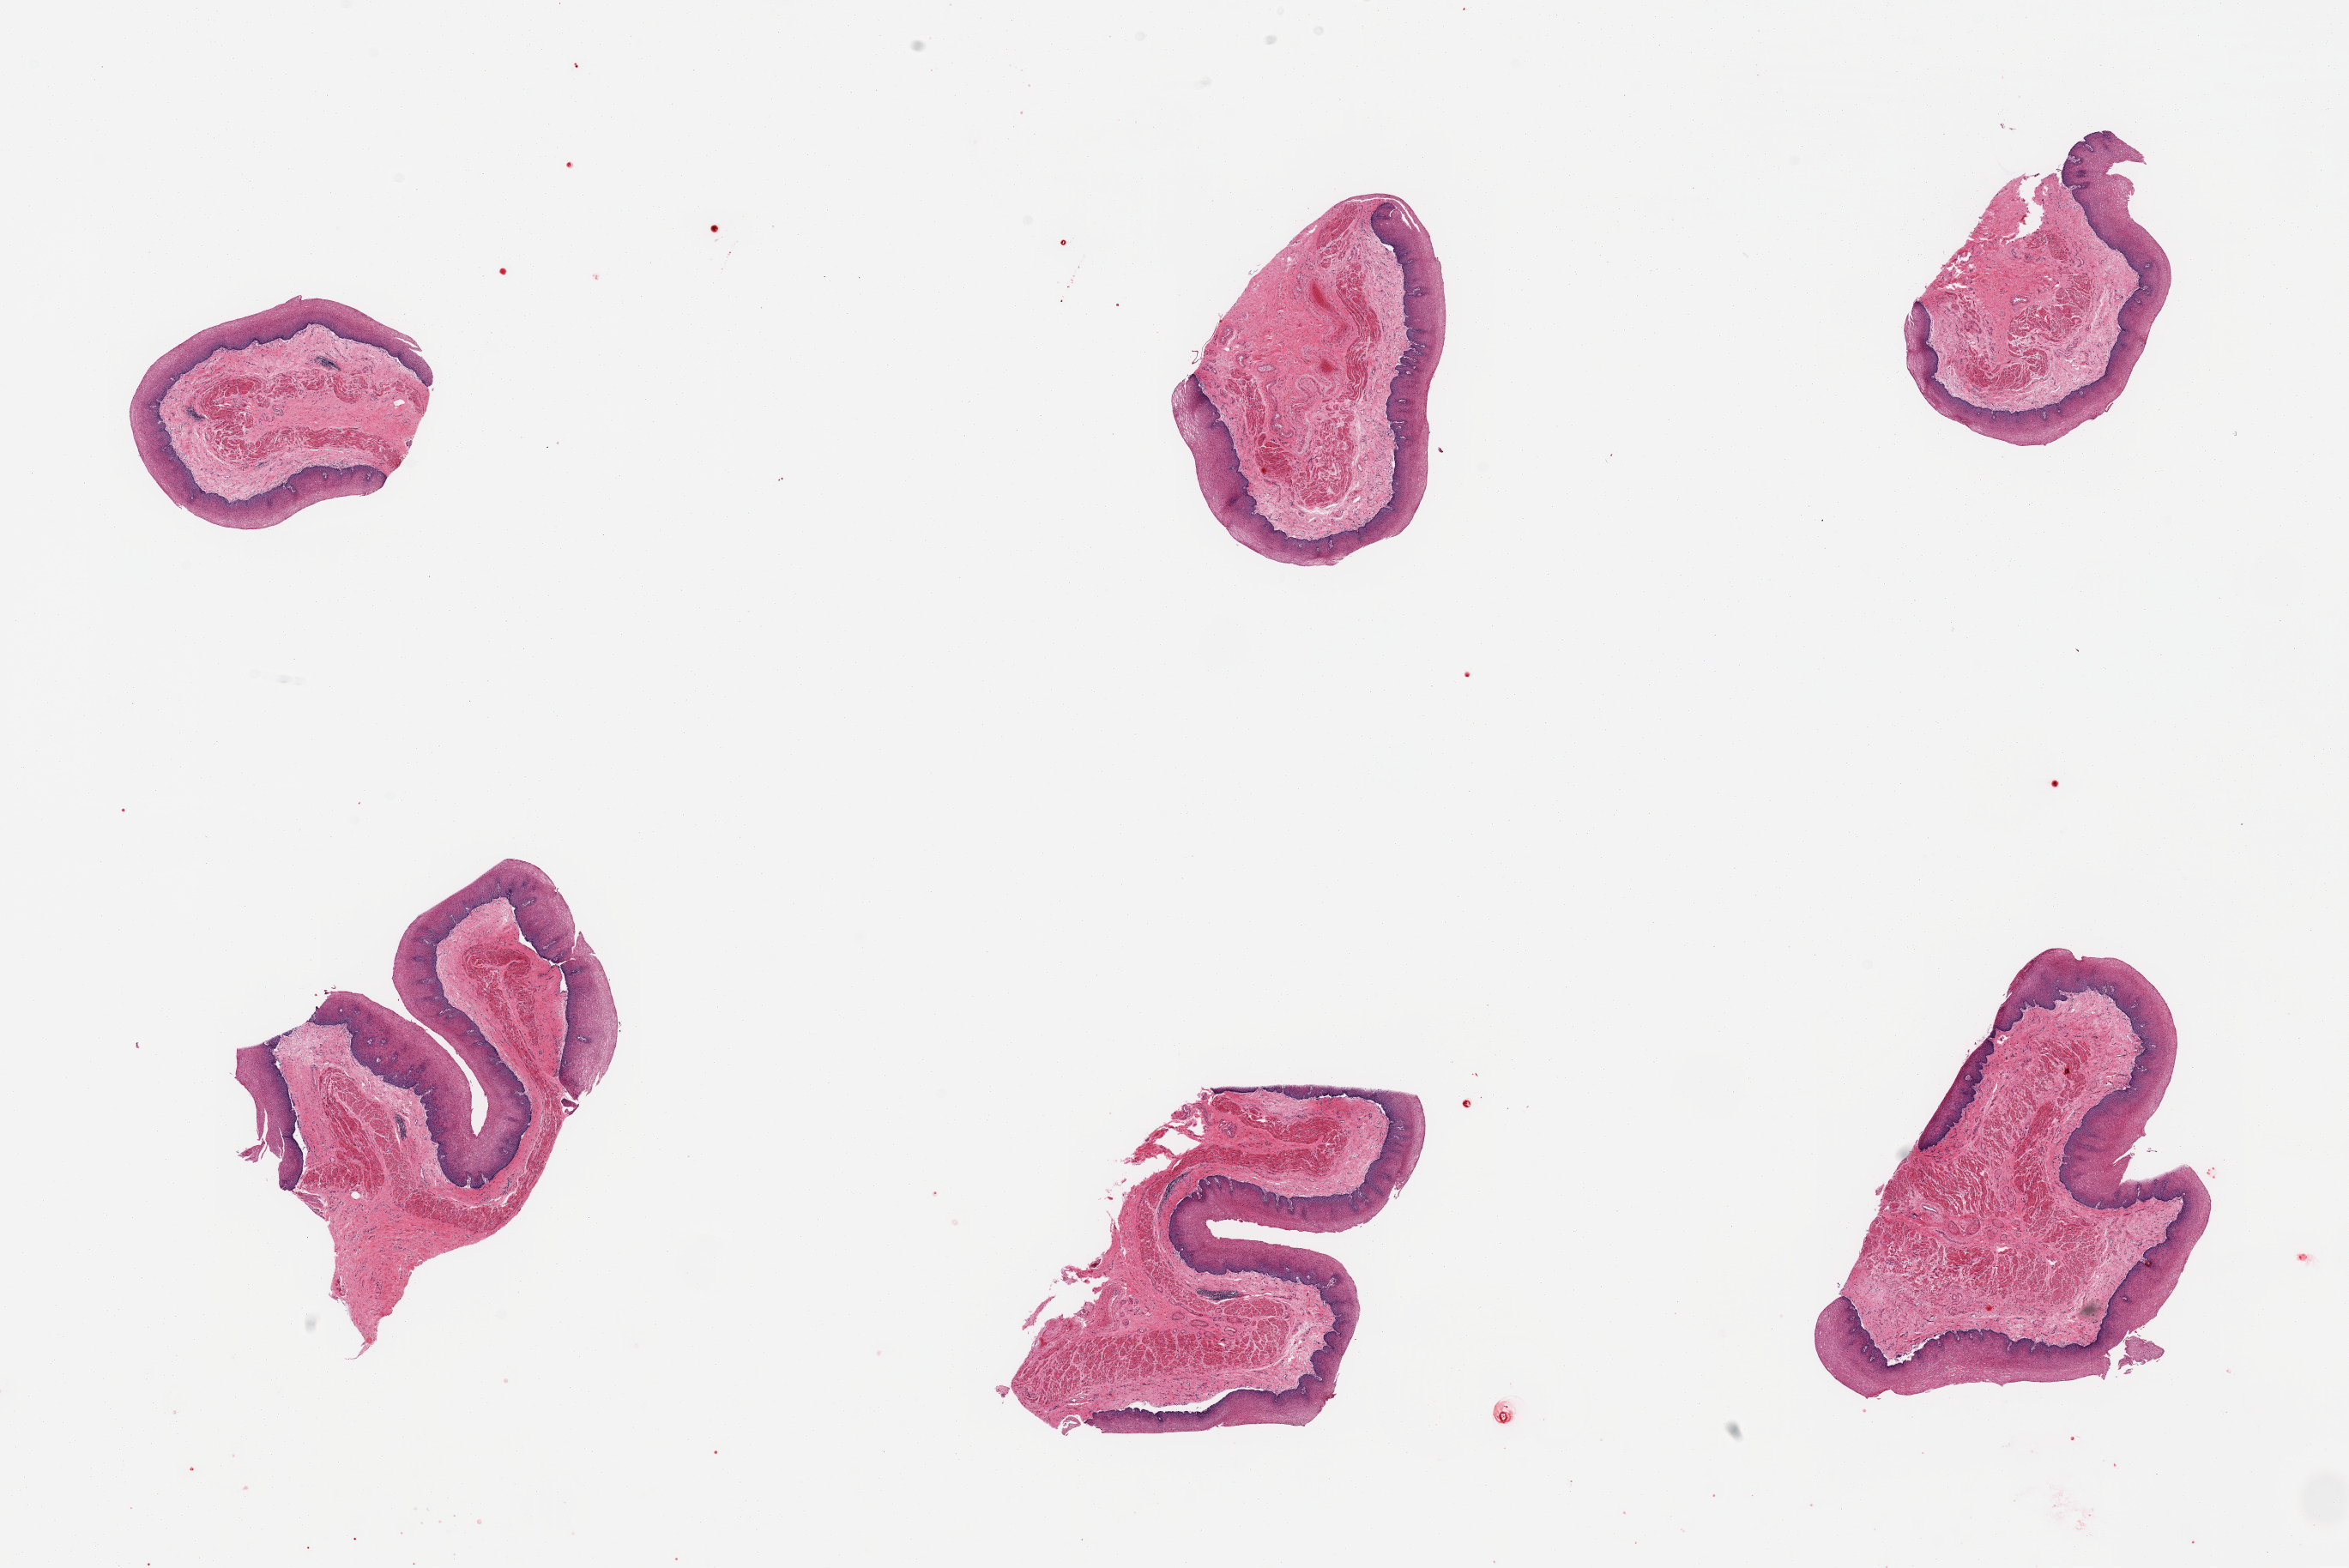
Digitized hematoxylin and eosin (H&E)-stained section — shown as a low-resolution overview of the whole scanned area (about 21.7 x 14.5 mm), PAXgene-fixed paraffin-embedded (PFPE) section, section of esophageal mucous membrane (target tissue), tissue donor sample. Donor sex: male.
Review note (as recorded): 6 pieces; well dissected mucosa with prominent muscularis mucosae.